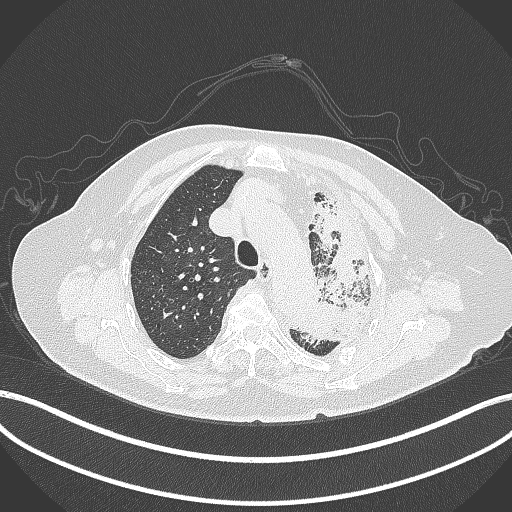
Chest CT, one axial slice. Position 298 of 399 along the scan axis. Reconstruction kernel B70f. 120 kVp. Lung window (W 1500 / L -600 HU). 1 mm slice thickness. 512 × 512 image matrix, field of view 400 × 400 mm. Patient: female, 75 years. Case-level facts recorded for this patient, not image findings: clinical TNM (as recorded): T3 N3 M1.
Structures marked on this image (rectangle marked by the reading radiologist):
- lung tumour (recorded histology: adenocarcinoma): bounding box [x1, y1, x2, y2] px = [287, 193, 368, 343]